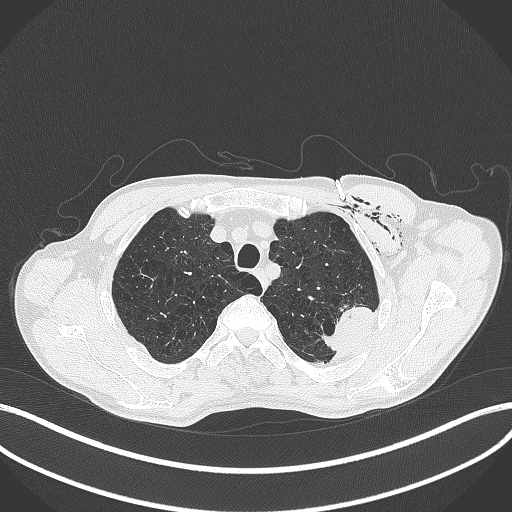
Chest CT, one axial slice. Position 345 of 457 along the scan axis. Lung window (W 1500 / L -600 HU). 512 × 512 image matrix, field of view 400 × 400 mm. Male patient, age 58 years. From the clinical record (not read from this slice): clinical TNM (as recorded): T3 N0 M0.
Structures marked on this image (rectangle marked by the reading radiologist):
- lung tumour (recorded histology: adenocarcinoma): bounding box <315,301,375,355> (left, top, right, bottom; pixels)